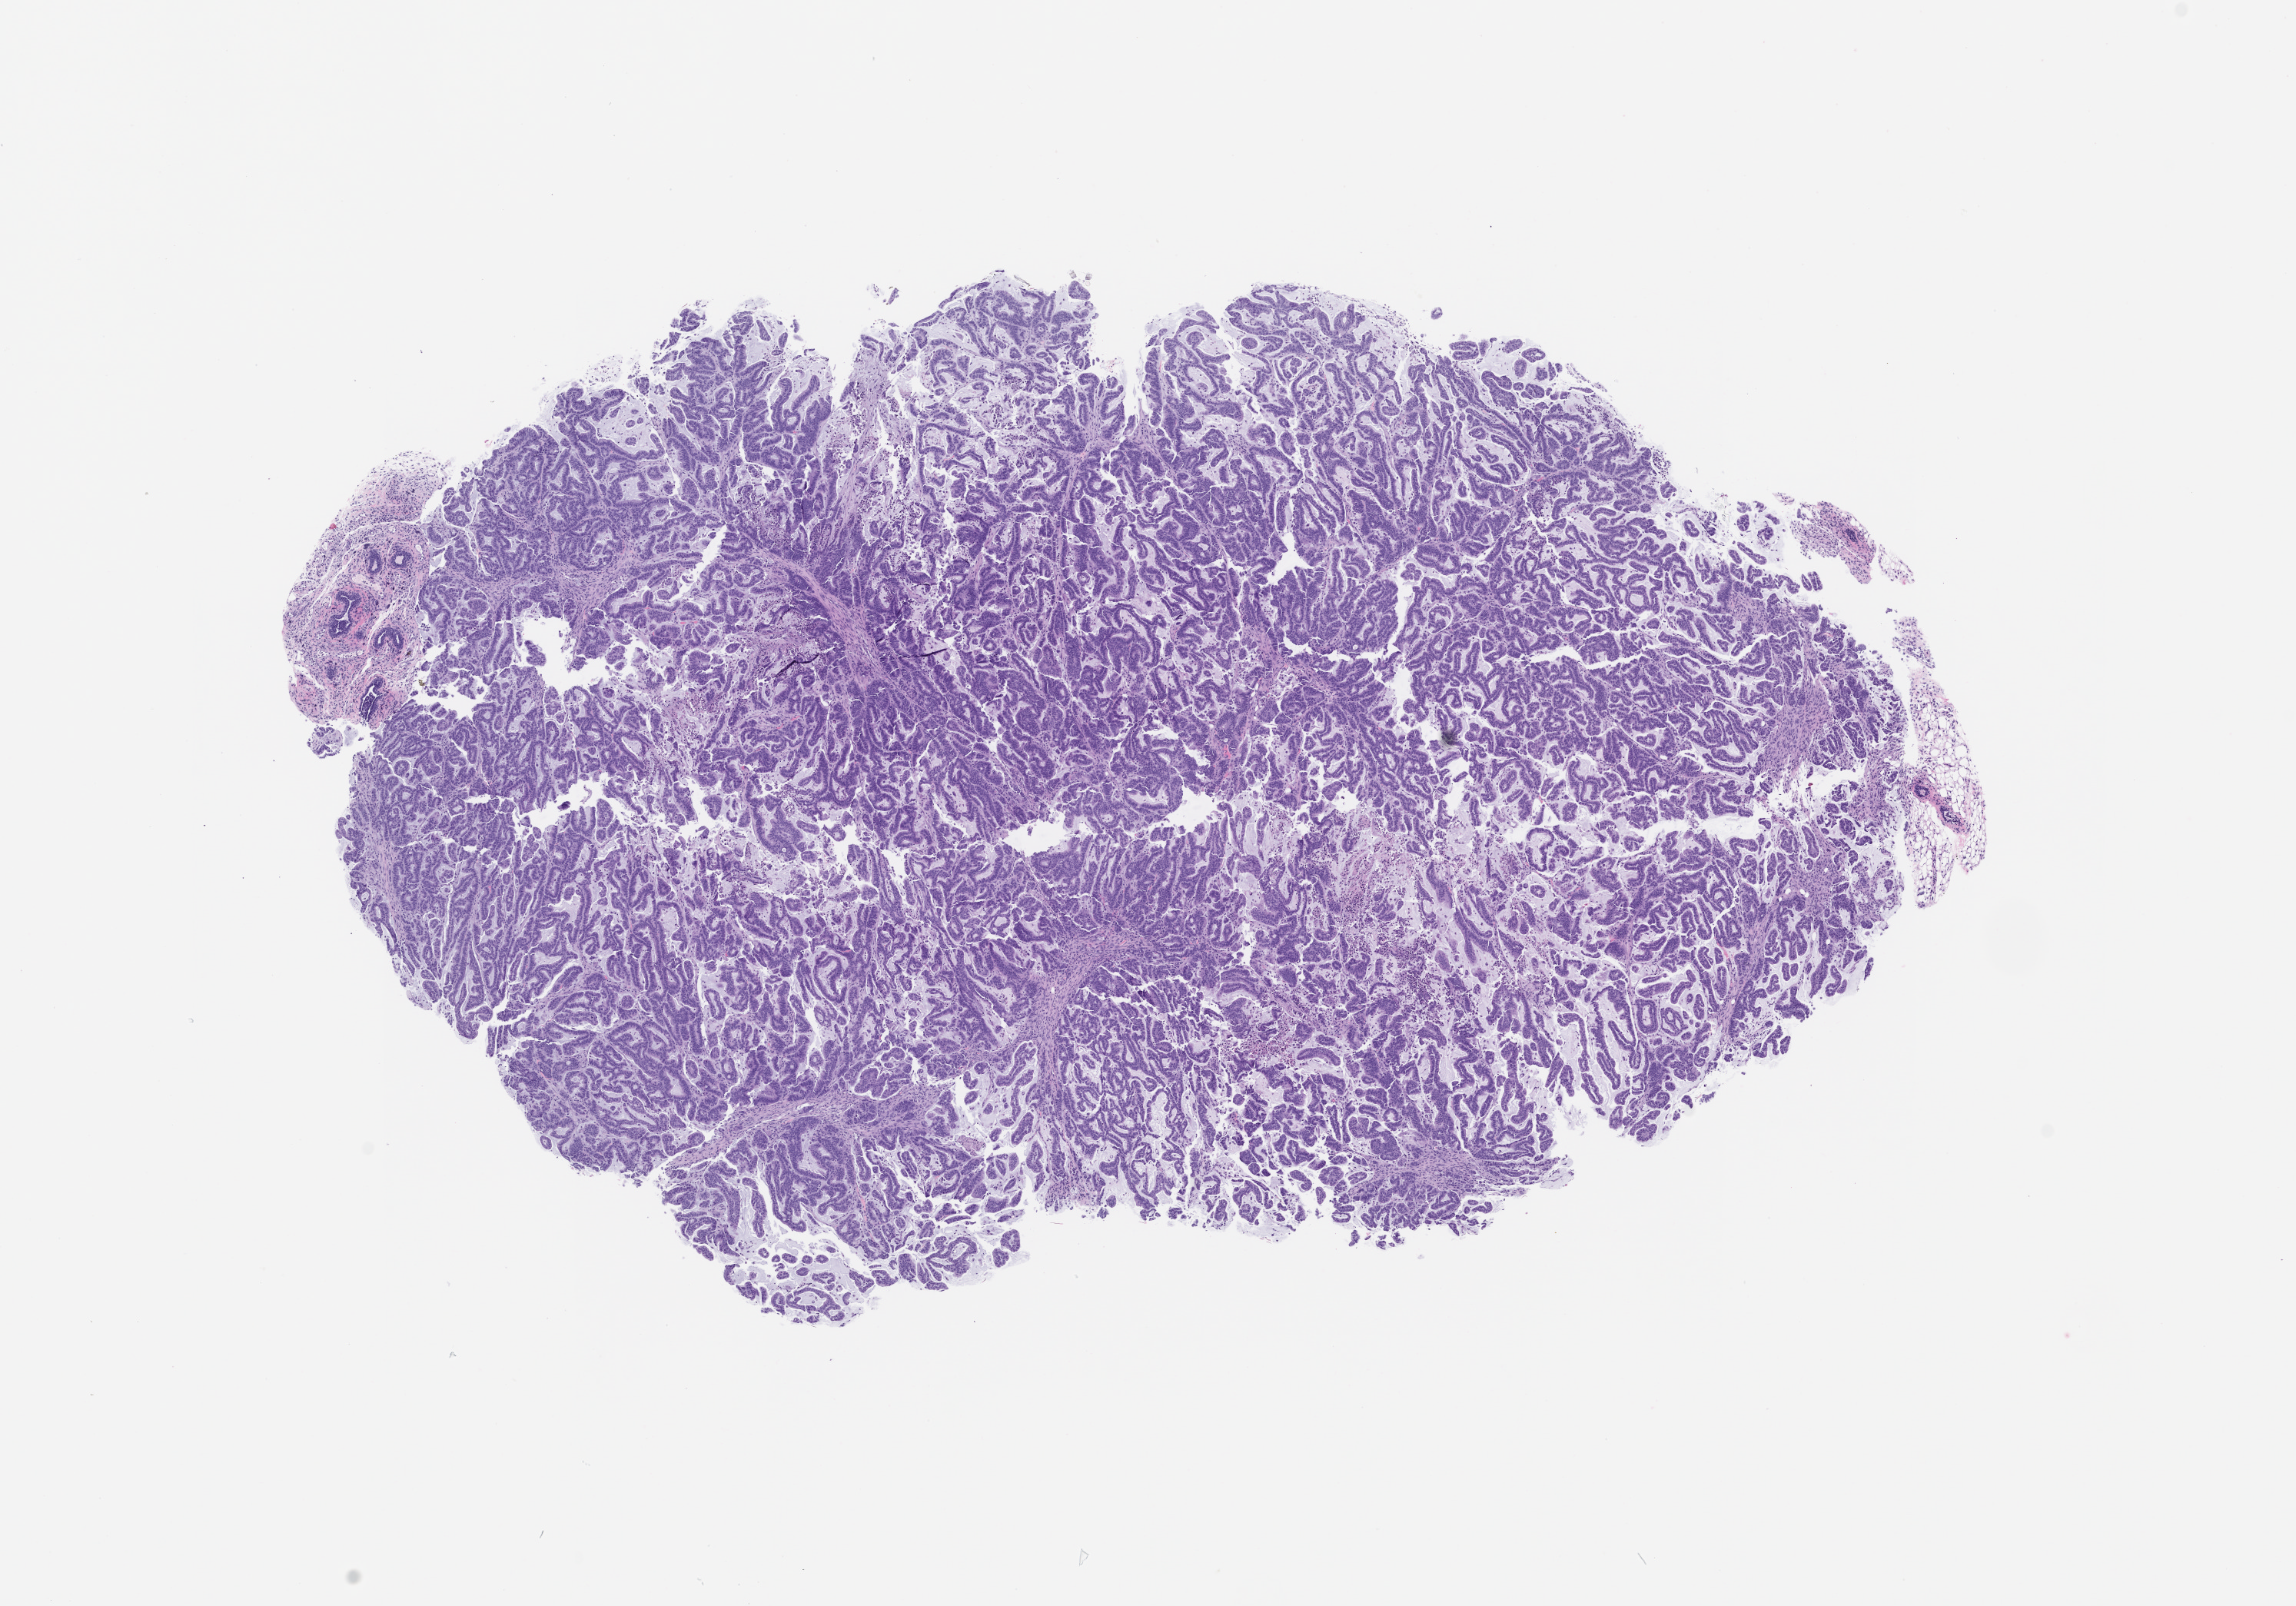
H&E whole-slide image of a patient-derived xenograft (PDX) tumor grown in a mouse, passage 0 — whole scanned area (about 12.0 x 8.4 mm) shown as a low-resolution overview; FFPE section; originating tumor site category: colon.
Originating patient diagnosis: Colon Adenocarcinoma.